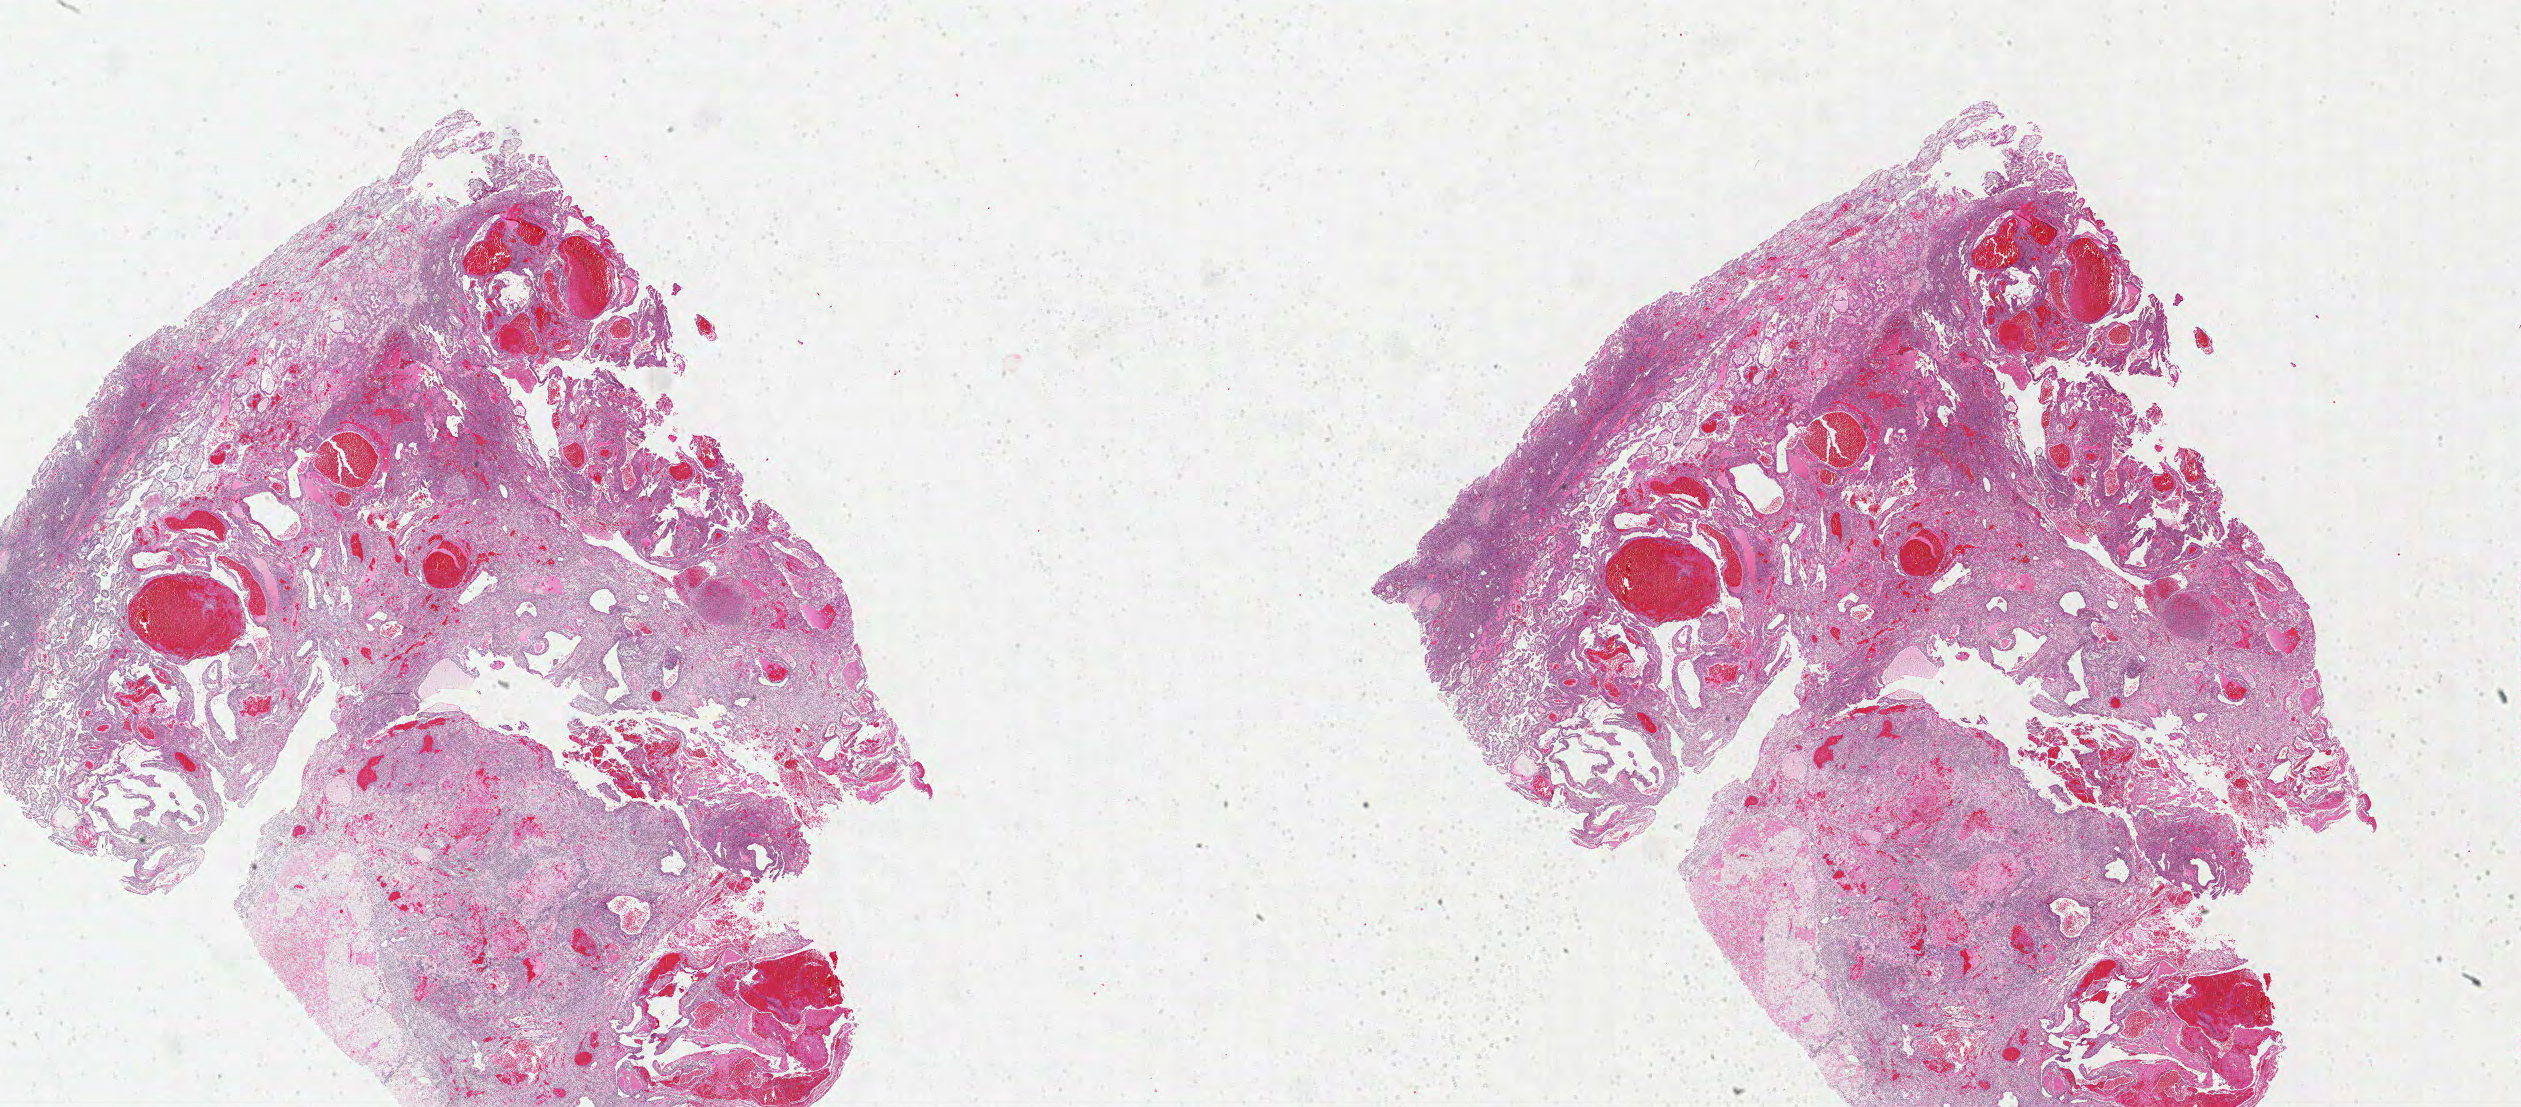
Digitized H&E tissue section (whole slide), shown as a low-resolution overview of the whole scanned area (about 39.6 x 17.4 mm); FFPE section; primary tumour sample from the kidney. Patient: male, age at initial diagnosis 63 years. Histologic grade: G3 (poorly differentiated).
• AJCC pathologic stage: I (7th edition)
• pathologic diagnosis: Clear cell adenocarcinoma, NOS
• TNM: T1b N0 M0
• laterality: left